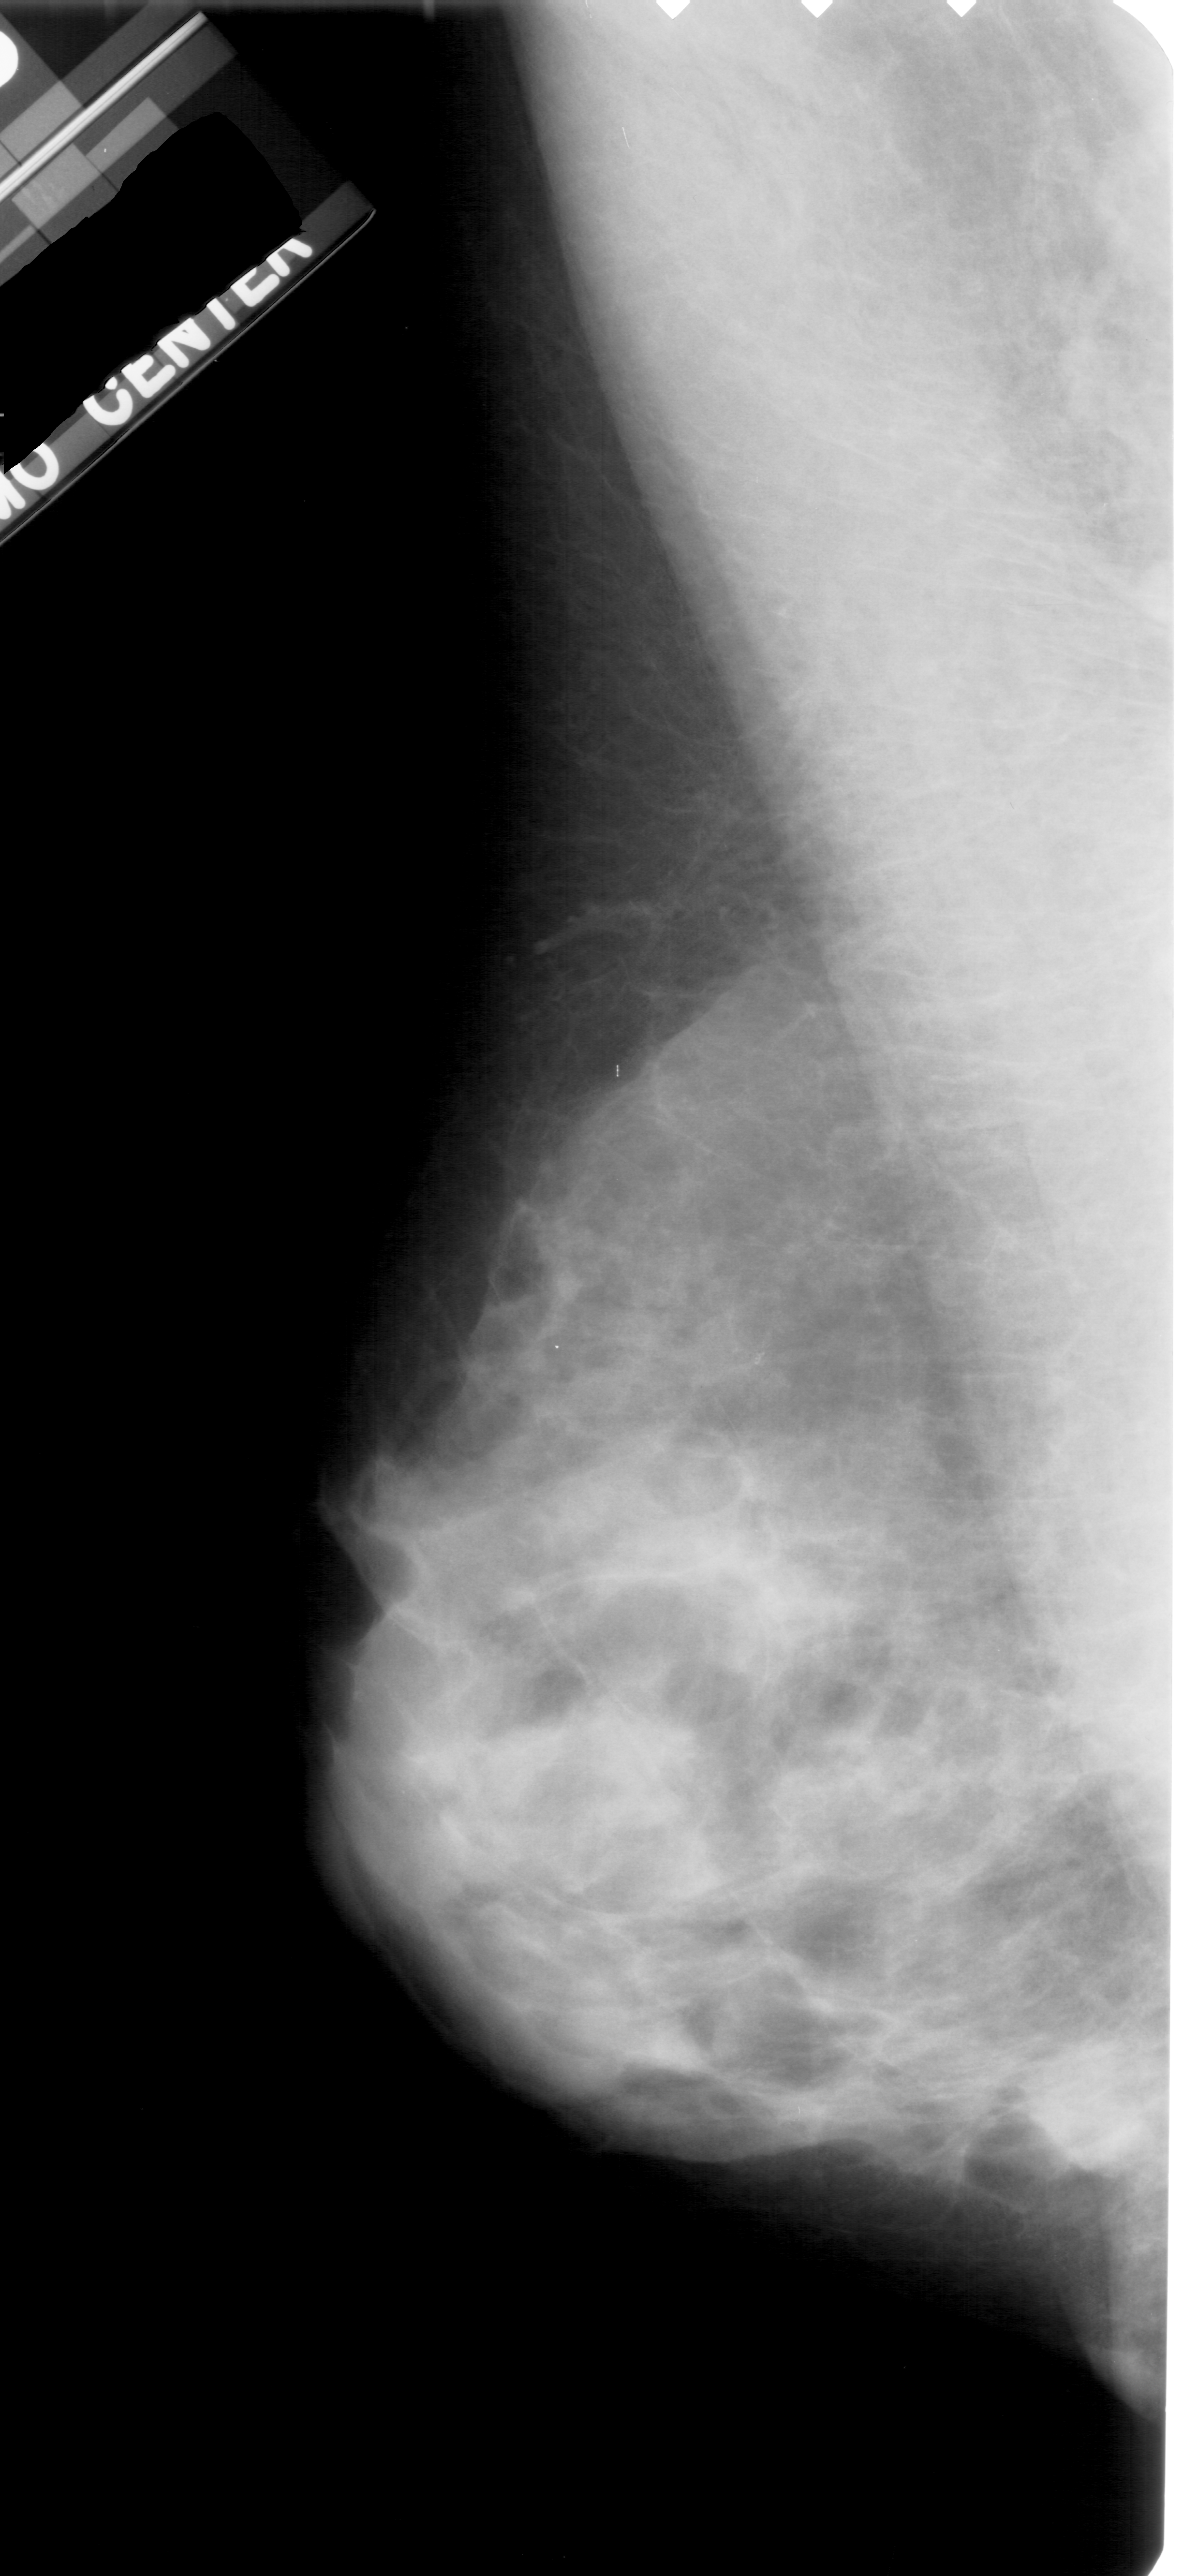
Scanned film-screen mammogram, left breast, mediolateral oblique (MLO) view, breast composition: extremely dense (BI-RADS density category 4 of 4).
Abnormality record for this image: calcifications, morphology pleomorphic, distribution clustered; BI-RADS assessment category 4; subtlety rating 2 on a 1 (subtle) to 5 (obvious) scale; pathology result (as recorded, not read from the image): benign.